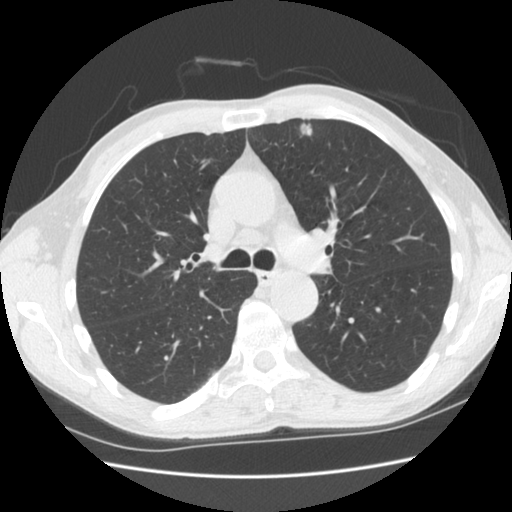
Low-dose screening chest CT, one axial slice; position 111 of 169 along the scan axis; 120 kVp; lung window (W 1500 / L -600 HU); 2.5 mm slice thickness; 512 × 512 image matrix, field of view 340 × 340 mm.
Outlined on this slice (outlined manually by an expert reader):
- lesion 1 (tumor, upper lobe of left lung): bounding box <299,122,312,137> (left, top, right, bottom; pixels)